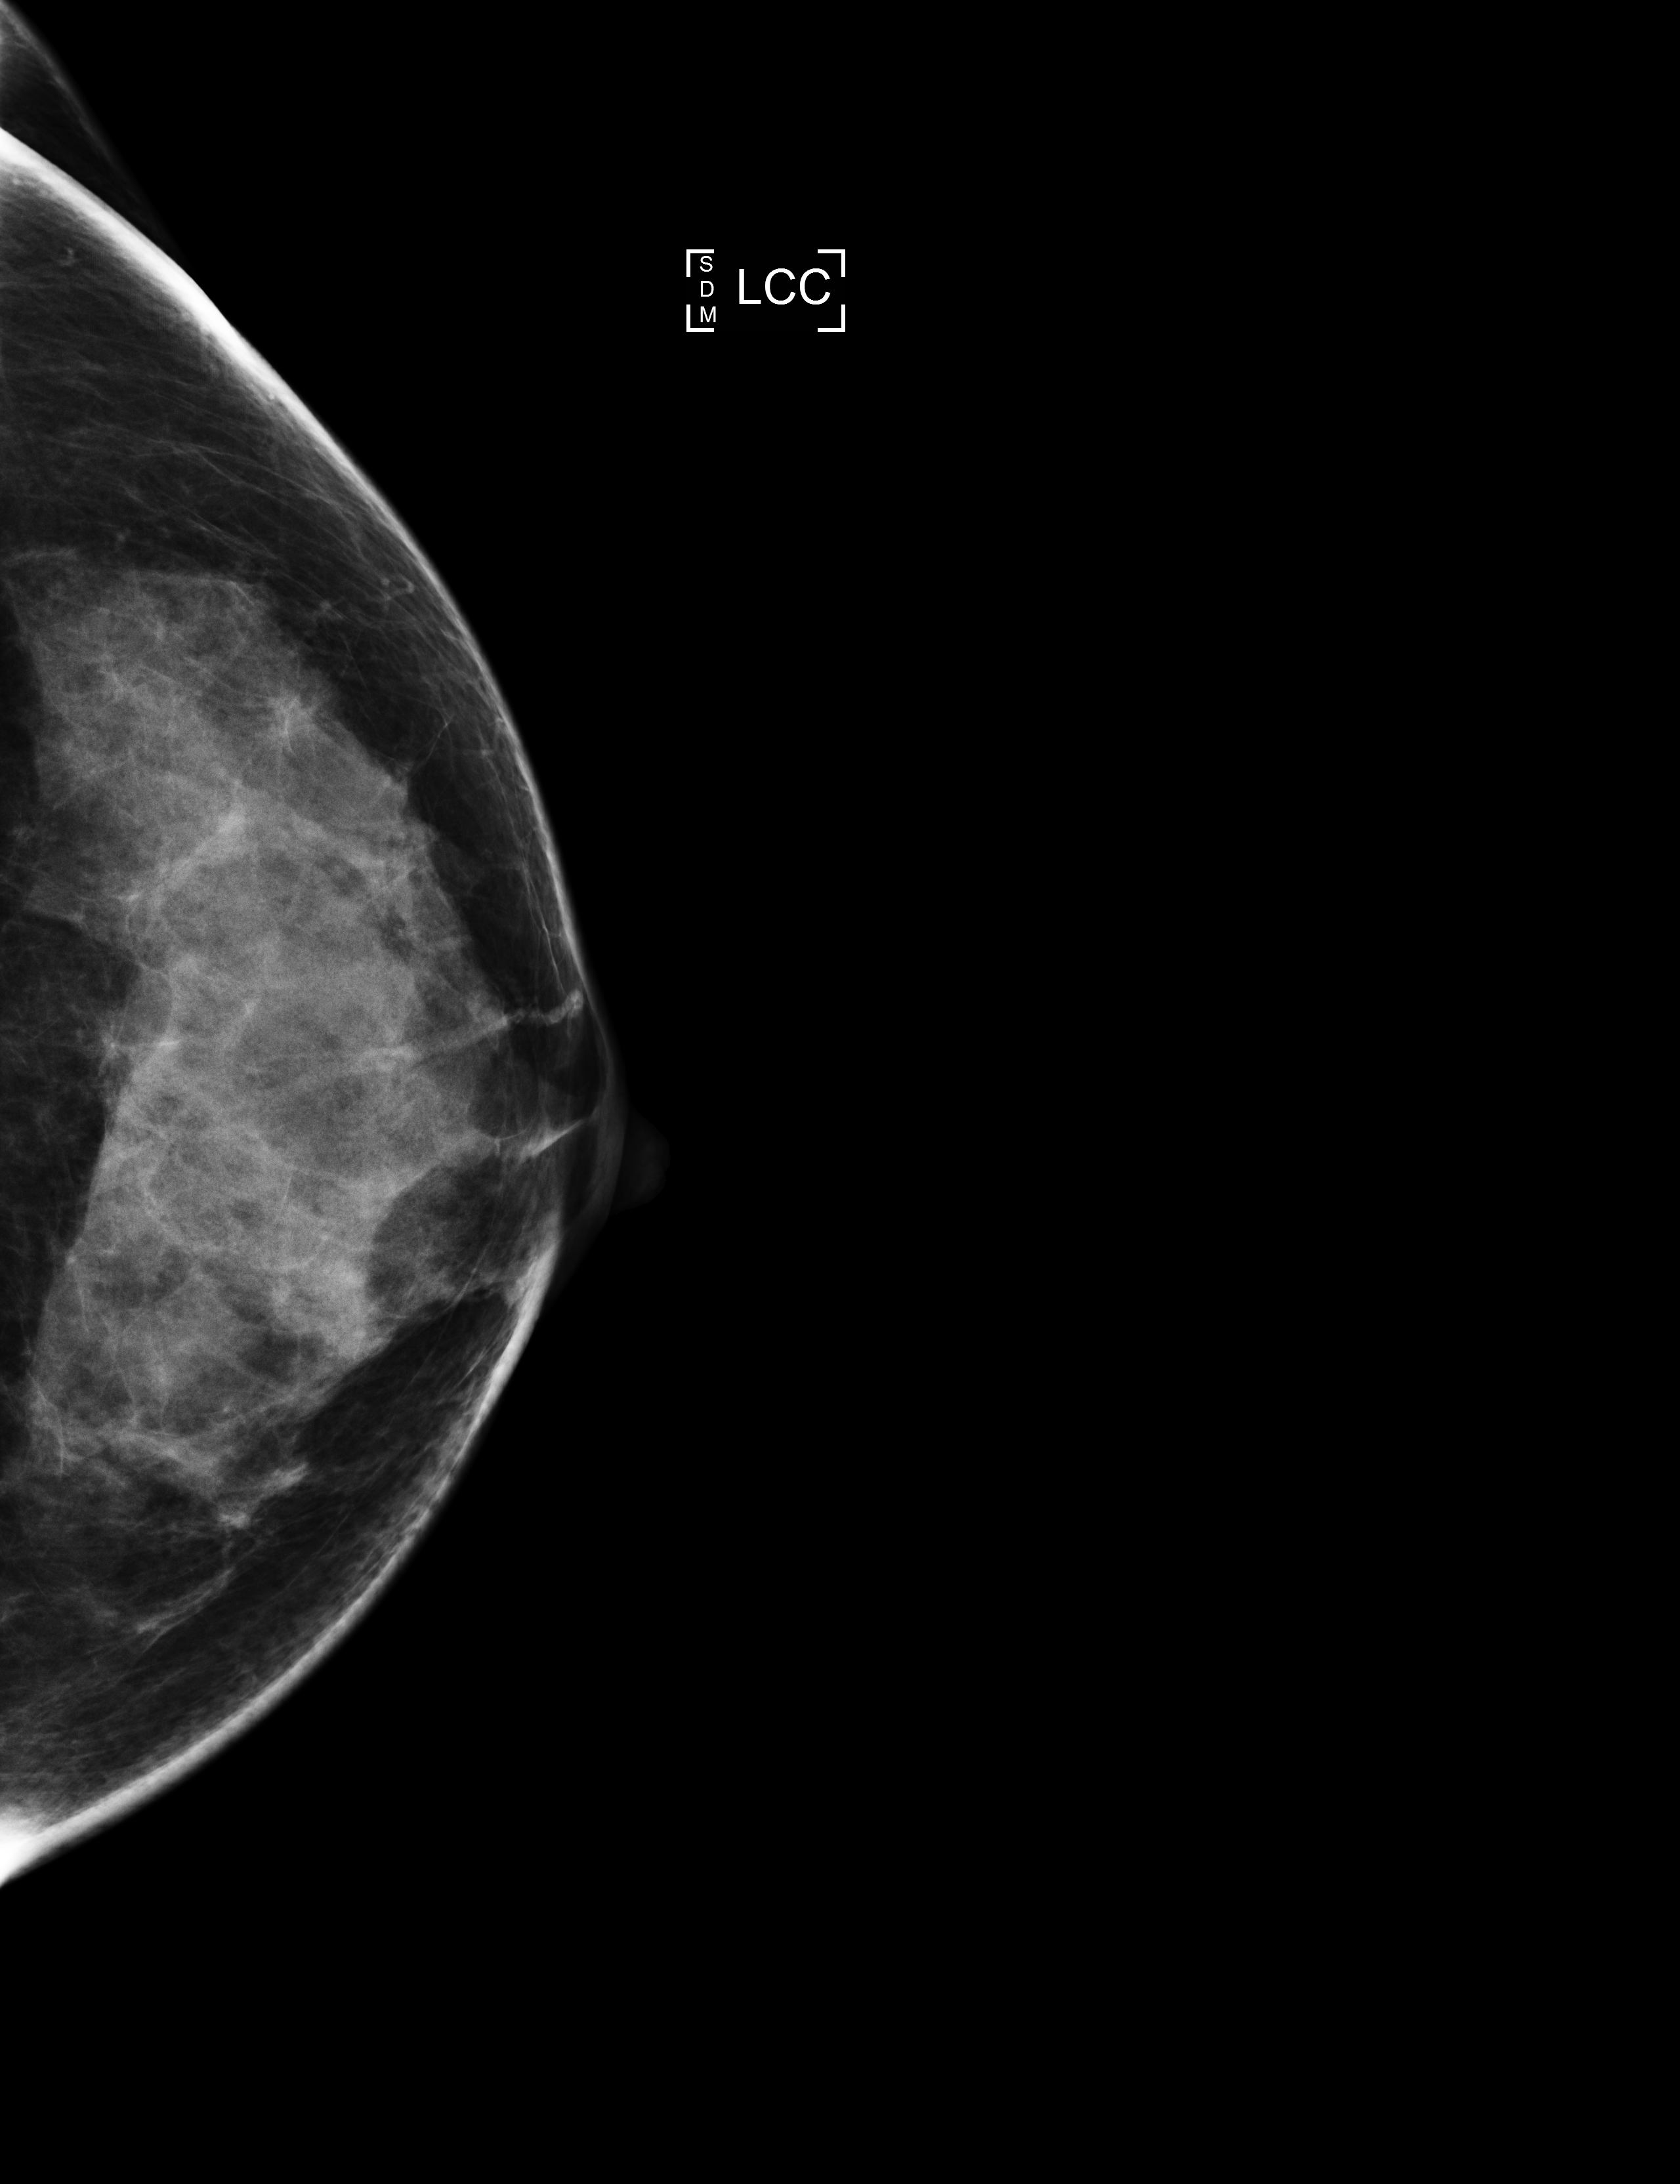
Digital mammogram (FFDM), left breast, CC view, annual screening mammography examination, compressed breast thickness 58 mm, system: Selenia Dimensions. Female patient, age 43 years.
BI-RADS breast density category at the screening exam (both breasts, scale 1–4): 3. Final BI-RADS assessment for this screening round (tomosynthesis exam, both breasts): category 1. Recall: recalled for additional imaging after this screen.